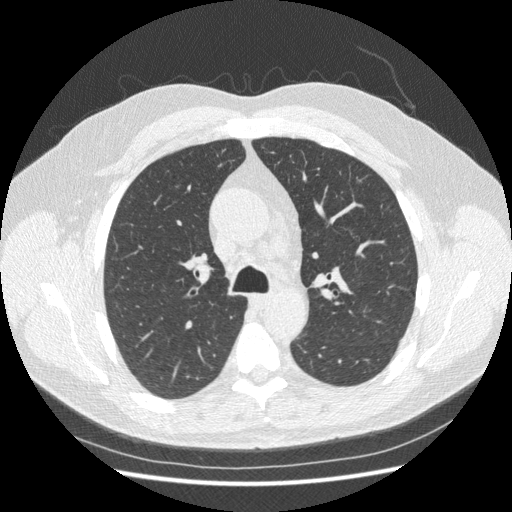
Low-dose screening chest CT, one axial slice. Lung window (W 1500 / L -600 HU). 1.25 mm slice thickness. 512 × 512 image matrix.
Annotated regions visible in this slice (outlined manually by an expert reader):
- lesion 1 (tumor, upper lobe of right lung): bounding box (x1, y1, x2, y2) in pixels: (175, 184, 182, 191)